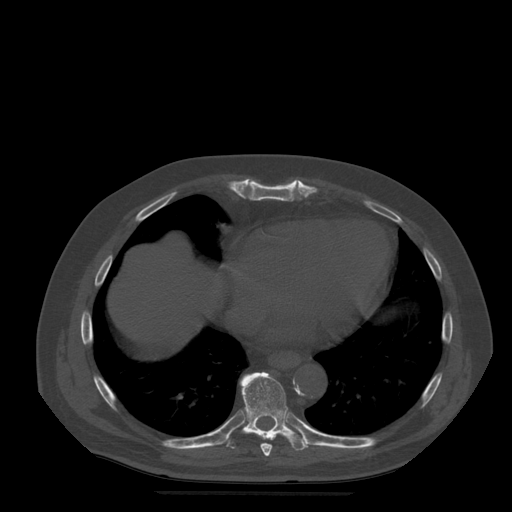
CT including the spine, one axial slice; bone window (W 1800 / L 400 HU); 1.25 mm slice thickness; 512 × 512 image matrix, field of view 420 × 420 mm. Patient age 72 years. Case-level facts recorded for this patient, not image findings: primary cancer: prostate.
Structures marked on this image (semi-automatic segmentation, software-assisted and operator-edited):
- T8 vertebra: bounding box (x1, y1, x2, y2) in pixels: (261, 443, 273, 457)
- T9 vertebra: (227, 372, 309, 451)